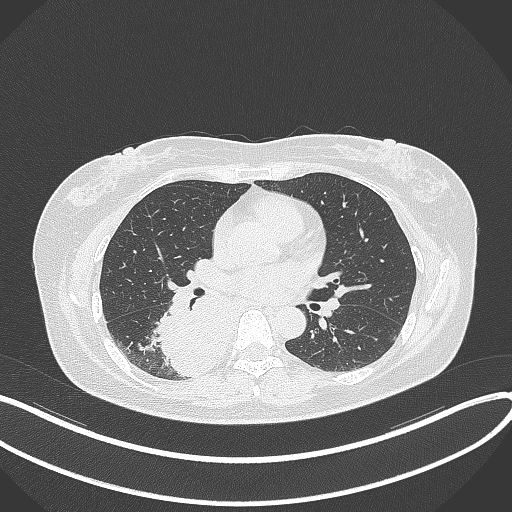
Chest CT, one axial slice. Position 186 of 331 along the scan axis. Reconstruction kernel B70f. Lung window (W 1500 / L -600 HU). 1 mm slice thickness. 512 × 512 image matrix, field of view 400 × 400 mm. Patient: female, 54 years. From the clinical record (not read from this slice): clinical TNM (as recorded): T4 N0 M0.
Structures marked on this image (rectangle marked by the reading radiologist):
- lung tumour (recorded histology: adenocarcinoma): box from (x=156, y=279) to (x=237, y=377) px